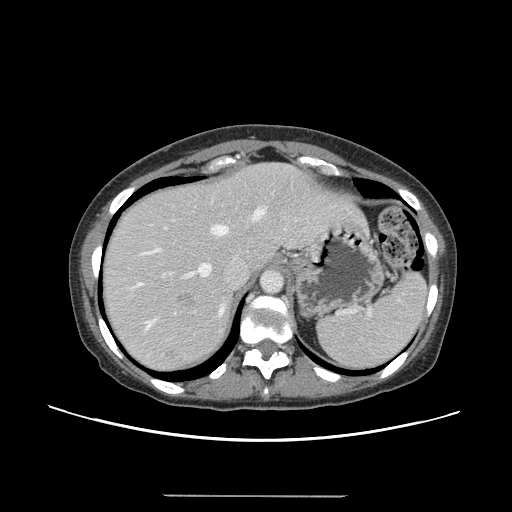
Contrast-enhanced abdominal CT, one axial slice. Slice 113 of 144 in the series (ordered by position). 120 kVp. Soft-tissue window (W 400 / L 40 HU). 2.5 mm slice thickness. 512 × 512 image matrix, field of view 380 × 380 mm. Female patient, age 53 years. From the clinical record (not read from this slice): diagnosis: colorectal cancer liver metastases, imaged before liver resection; multiple liver metastases: yes; largest metastasis: 1.1 cm; chemotherapy before resection: no.
Structures marked on this image (manually delineated by an expert):
- hepatic veins: bounding box [x1, y1, x2, y2] px = [137, 208, 265, 329]
- liver: [103, 164, 361, 371]
- planned liver remnant (the part of the liver to remain after resection): [102, 164, 292, 300]
- portal vein (with intrahepatic branches): [162, 220, 174, 278]
- liver metastasis: [177, 294, 192, 303]
- liver metastasis: [165, 352, 174, 361]